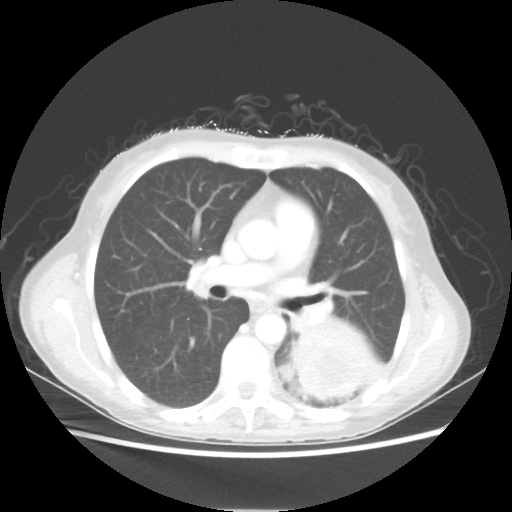
Chest CT, one axial slice. Position 31 of 56 along the scan axis. Reconstruction kernel STANDARD. Lung window (W 1500 / L -600 HU). 5 mm slice thickness. 512 × 512 image matrix, field of view 360 × 360 mm. Patient: female, 53 years. From the clinical record (not read from this slice): clinical TNM (as recorded): T3 N0 M0.
Outlined on this slice (rectangle marked by the reading radiologist):
- lung tumour (recorded histology: adenocarcinoma): bounding box <294,321,383,400> (left, top, right, bottom; pixels)